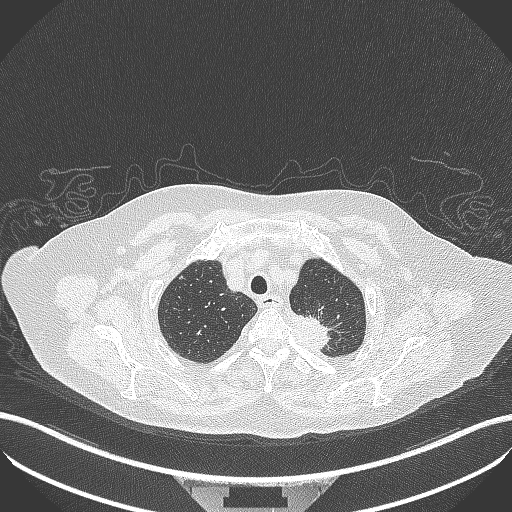
Chest CT, one axial slice. Position 293 of 353 along the scan axis. Reconstruction kernel B70f. Lung window (W 1500 / L -600 HU). 512 × 512 image matrix, field of view 400 × 400 mm. Female patient, age 81 years. Case-level facts recorded for this patient, not image findings: clinical TNM (as recorded): T2a N0 M0.
Outlined on this slice (bounding box drawn by a radiologist):
- lung tumour (recorded histology: adenocarcinoma): bounding box <281,310,341,351> (left, top, right, bottom; pixels)